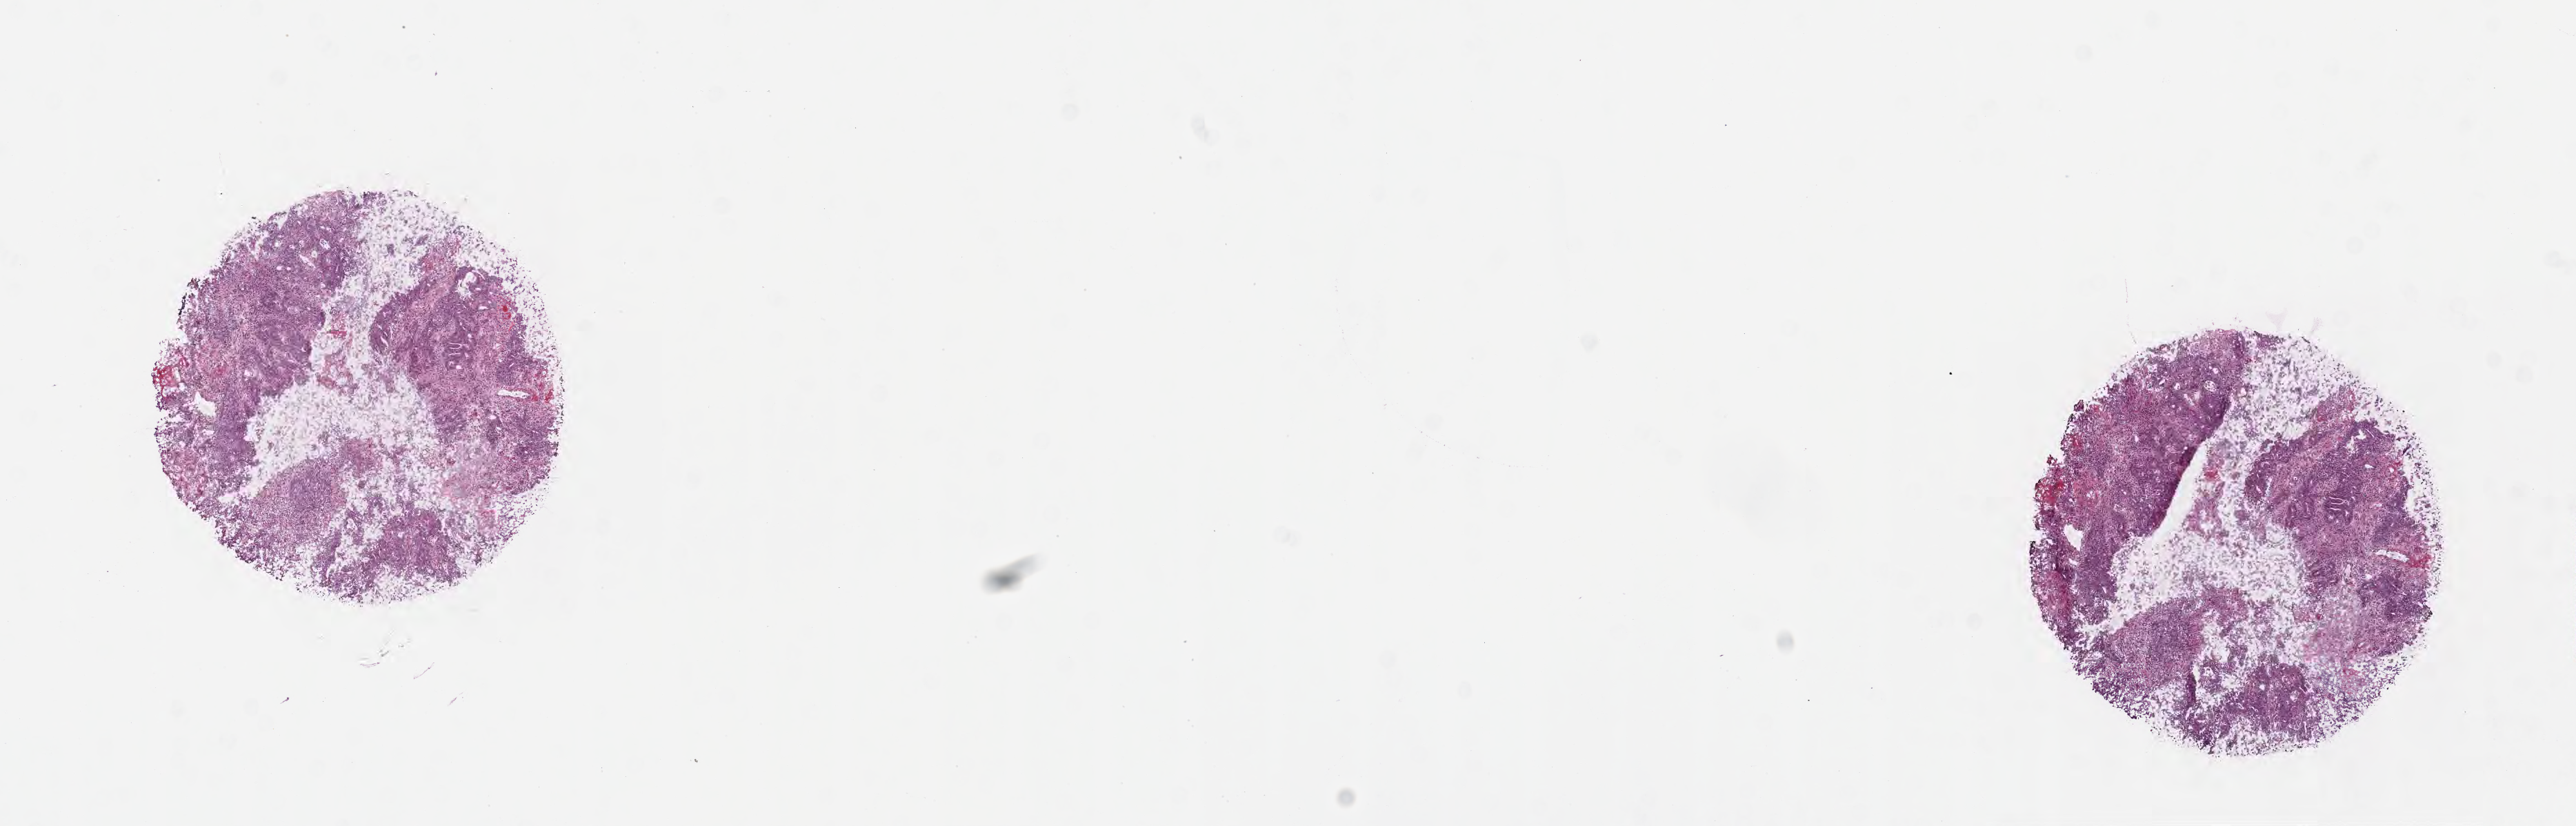
Whole-slide image, H&E stain — whole scanned area (about 15.1 x 4.8 mm) shown as a low-resolution overview; cryosection; specimen: primary tumor; anatomic site: cecum. Male patient; age at initial diagnosis 74 years. Tumor grade: GB (borderline). Pathologist review of this section (percent, as recorded): tumor cells 80%, tumor nuclei 80%, stromal cells 20%, necrosis 0%, normal cells 0%. Infiltration values recorded for this section: lymphocyte infiltration 4%, monocyte infiltration 3%, neutrophil infiltration 7%.
• AJCC pathologic stage: Stage IIIB
• histologic diagnosis: Adenocarcinoma, NOS